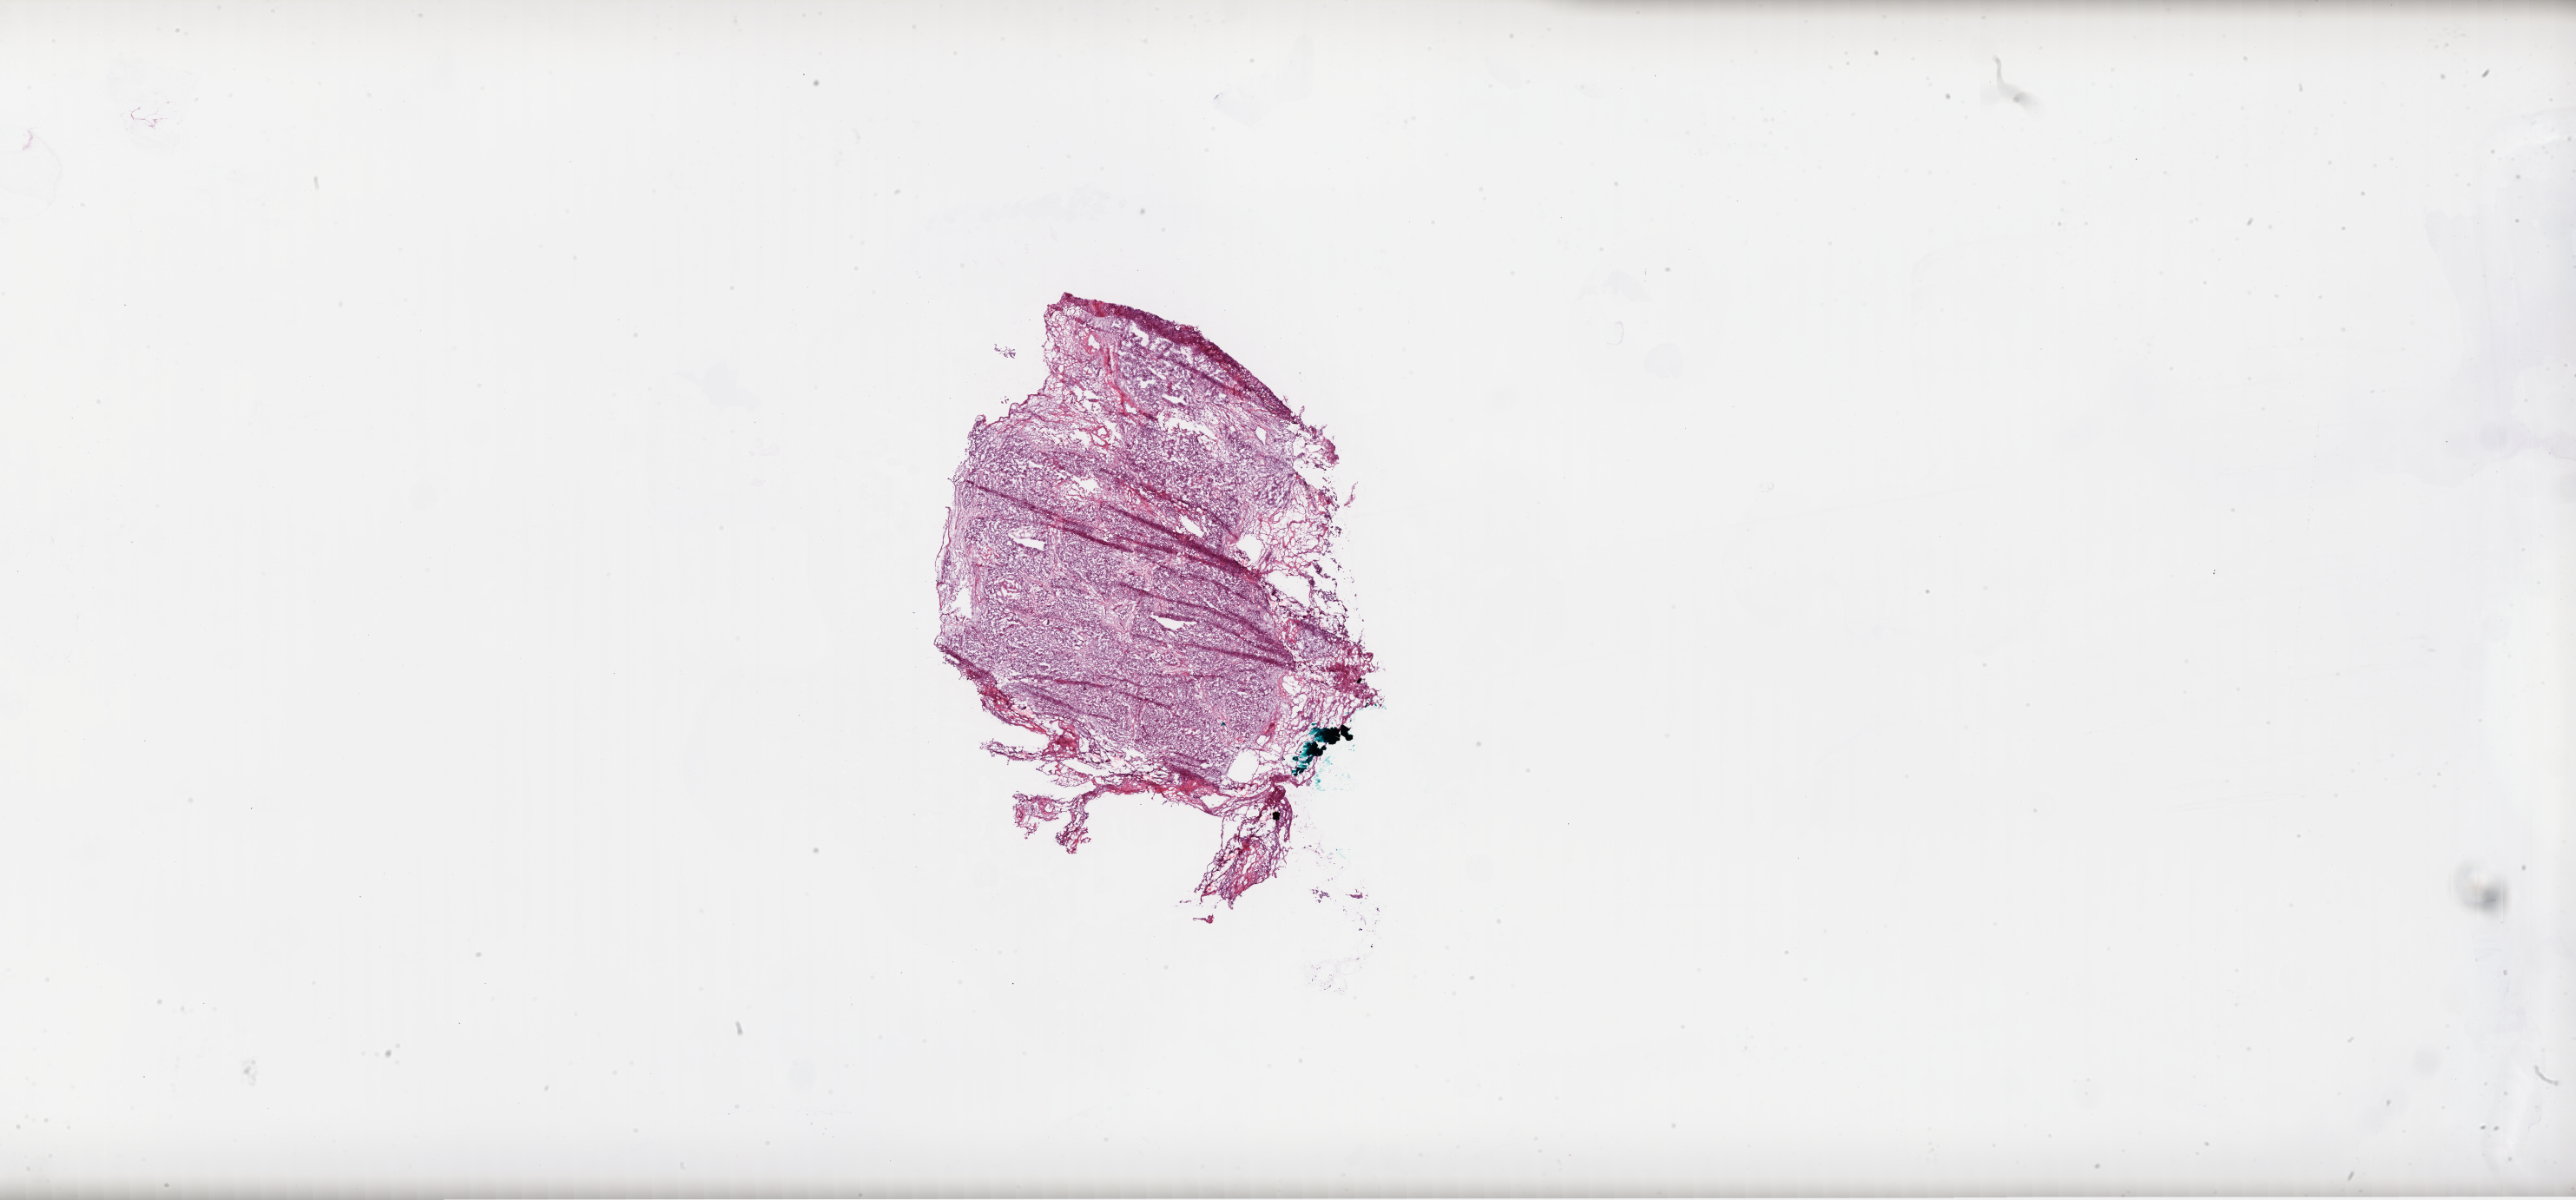
Hematoxylin and eosin (H&E) stained whole-slide image — whole scanned area (about 47.9 x 22.3 mm) shown as a low-resolution overview. Frozen section from the bottom of the tissue portion. Ovary, primary tumour sample. Female patient; age at initial diagnosis 58 years. Histologic grade: G3 (poorly differentiated). Pathologist review of this section (percent, as recorded): tumour cells 80%, tumour nuclei 85%, normal cells 0%, stromal cells 20%, necrosis 0%.
Laterality: bilateral. Histologic diagnosis: Serous cystadenocarcinoma, NOS. FIGO stage: IIIC.